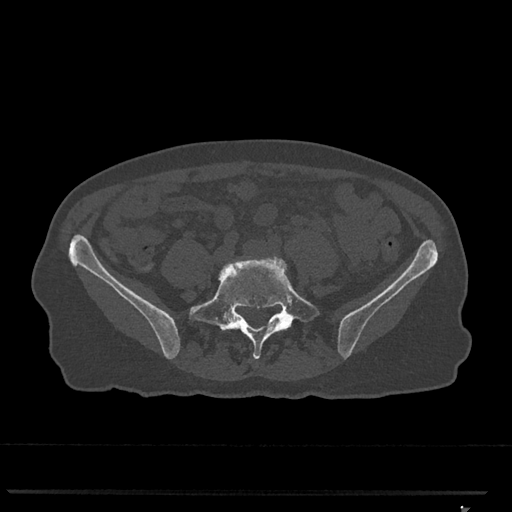
CT including the spine, one axial slice. Slice 156 of 793 in the series (ordered by position). 120 kVp. Bone window (W 1800 / L 400 HU). 0.5 mm slice thickness. 512 × 512 image matrix, field of view 380 × 380 mm. Patient: female, 62 years. From the clinical record (not read from this slice): primary cancer: renal.
Outlined on this slice (semi-automatic segmentation, software-assisted and operator-edited):
- L4 vertebra: bounding box (x1, y1, x2, y2) in pixels: (219, 259, 260, 274)
- L5 vertebra: (189, 257, 320, 359)